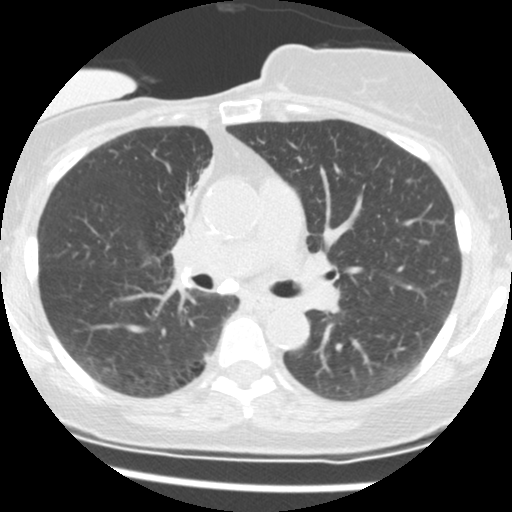
Low-dose screening chest CT, axial slice, second screening round (one year after baseline), lung window (W 1500 / L -600 HU), standard (soft-tissue) reconstruction kernel (STANDARD). Female, age 56 years at enrolment. Current smoker at enrolment.
- Lesion marked by an expert reader, box from (x=151, y=154) to (x=205, y=252) px.
- The screening reader recorded 2 non-calcified nodules or masses ≥4 mm on this exam (right middle lobe, right lower lobe); which of them this box marks is not recorded.
- Lung cancer was diagnosed 675 days after this screen: adenocarcinoma, NOS, right upper lobe, stage IIIB (AJCC 6th edition), 8 mm at pathology.